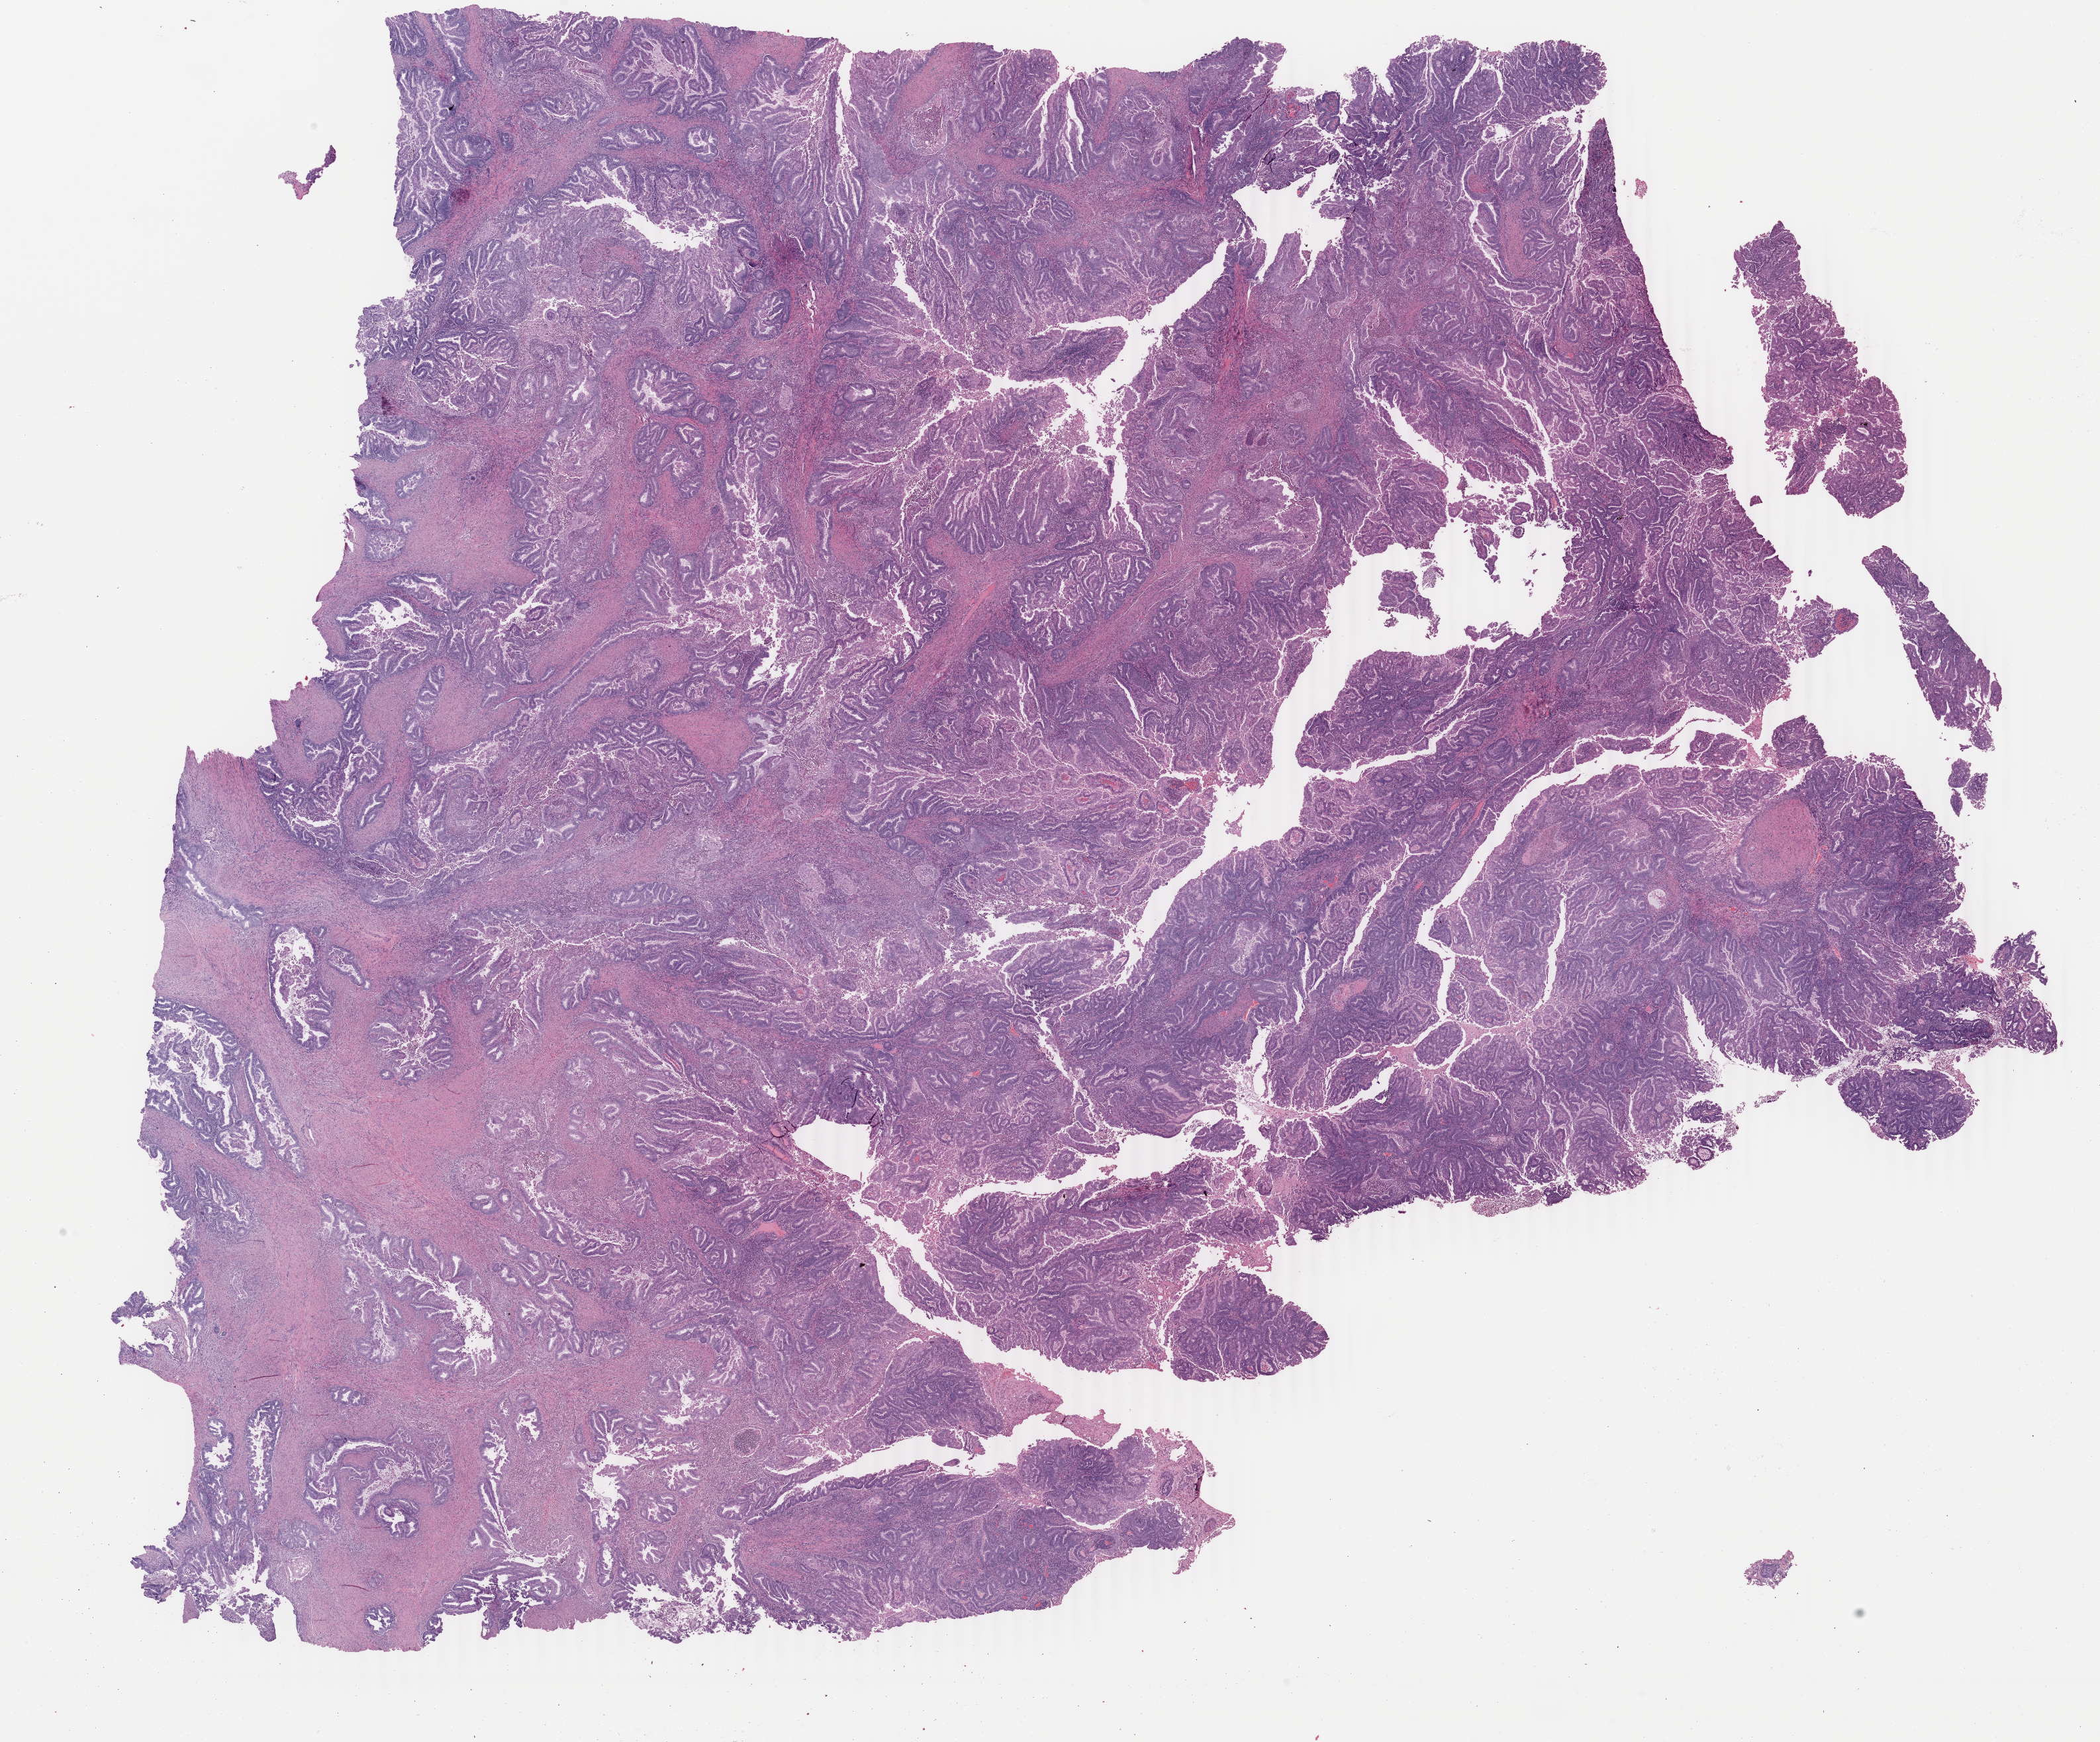
Hematoxylin and eosin (H&E) stained whole-slide image, a low-resolution overview of the entire scanned area, about 25.2 x 20.9 mm (slide scanned at 40x); formalin-fixed paraffin-embedded (FFPE) diagnostic section; sample: primary tumour, uterus. Female patient; age at initial diagnosis 61 years. Histologic grade: G2 (moderately differentiated).
FIGO stage: IC. Histologic diagnosis: Endometrioid adenocarcinoma, NOS (endometrium).